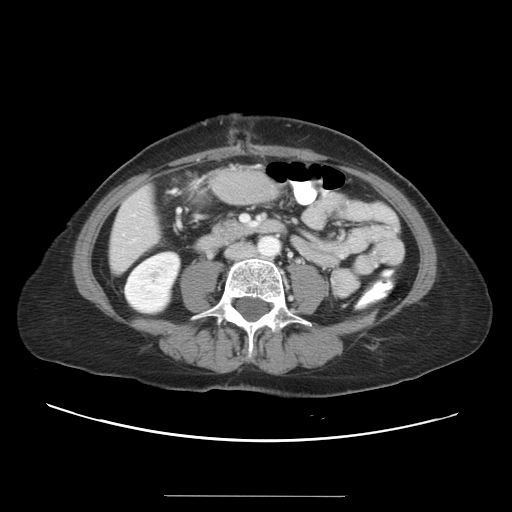
Contrast-enhanced abdominal CT, one axial slice; 120 kVp; intravenous contrast given; soft-tissue window (W 400 / L 40 HU); 5 mm slice thickness; 512 × 512 image matrix. Female patient, age 69 years. Case-level facts recorded for this patient, not image findings: diagnosis: colorectal cancer liver metastases, imaged before liver resection; multiple liver metastases: yes; largest metastasis: 1.4 cm; disease in both lobes: yes.
Annotated regions visible in this slice (outlined manually by an expert reader):
- liver: bounding box <110,188,160,272> (left, top, right, bottom; pixels)
- planned liver remnant (the part of the liver to remain after resection): <110,223,159,272>
- portal vein (with intrahepatic branches): <241,216,249,222>